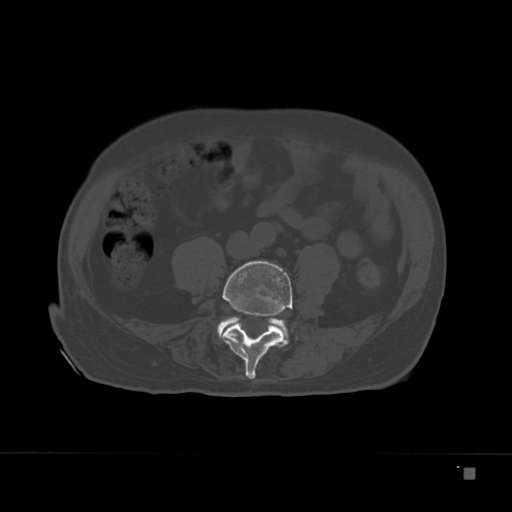
CT including the spine, one axial slice. Slice 40 of 332 in the series (ordered by position). Reconstruction kernel Br40s. 120 kVp. Bone window (W 1800 / L 400 HU). 1.5 mm slice thickness. 512 × 512 image matrix. Patient: male, 72 years. Case-level facts recorded for this patient, not image findings: primary cancer: skeletal.
Structures marked on this image (semi-automatic segmentation, software-assisted and operator-edited):
- L4 vertebra: bounding box <224,260,293,380> (left, top, right, bottom; pixels)
- L5 vertebra: <217,317,292,344>